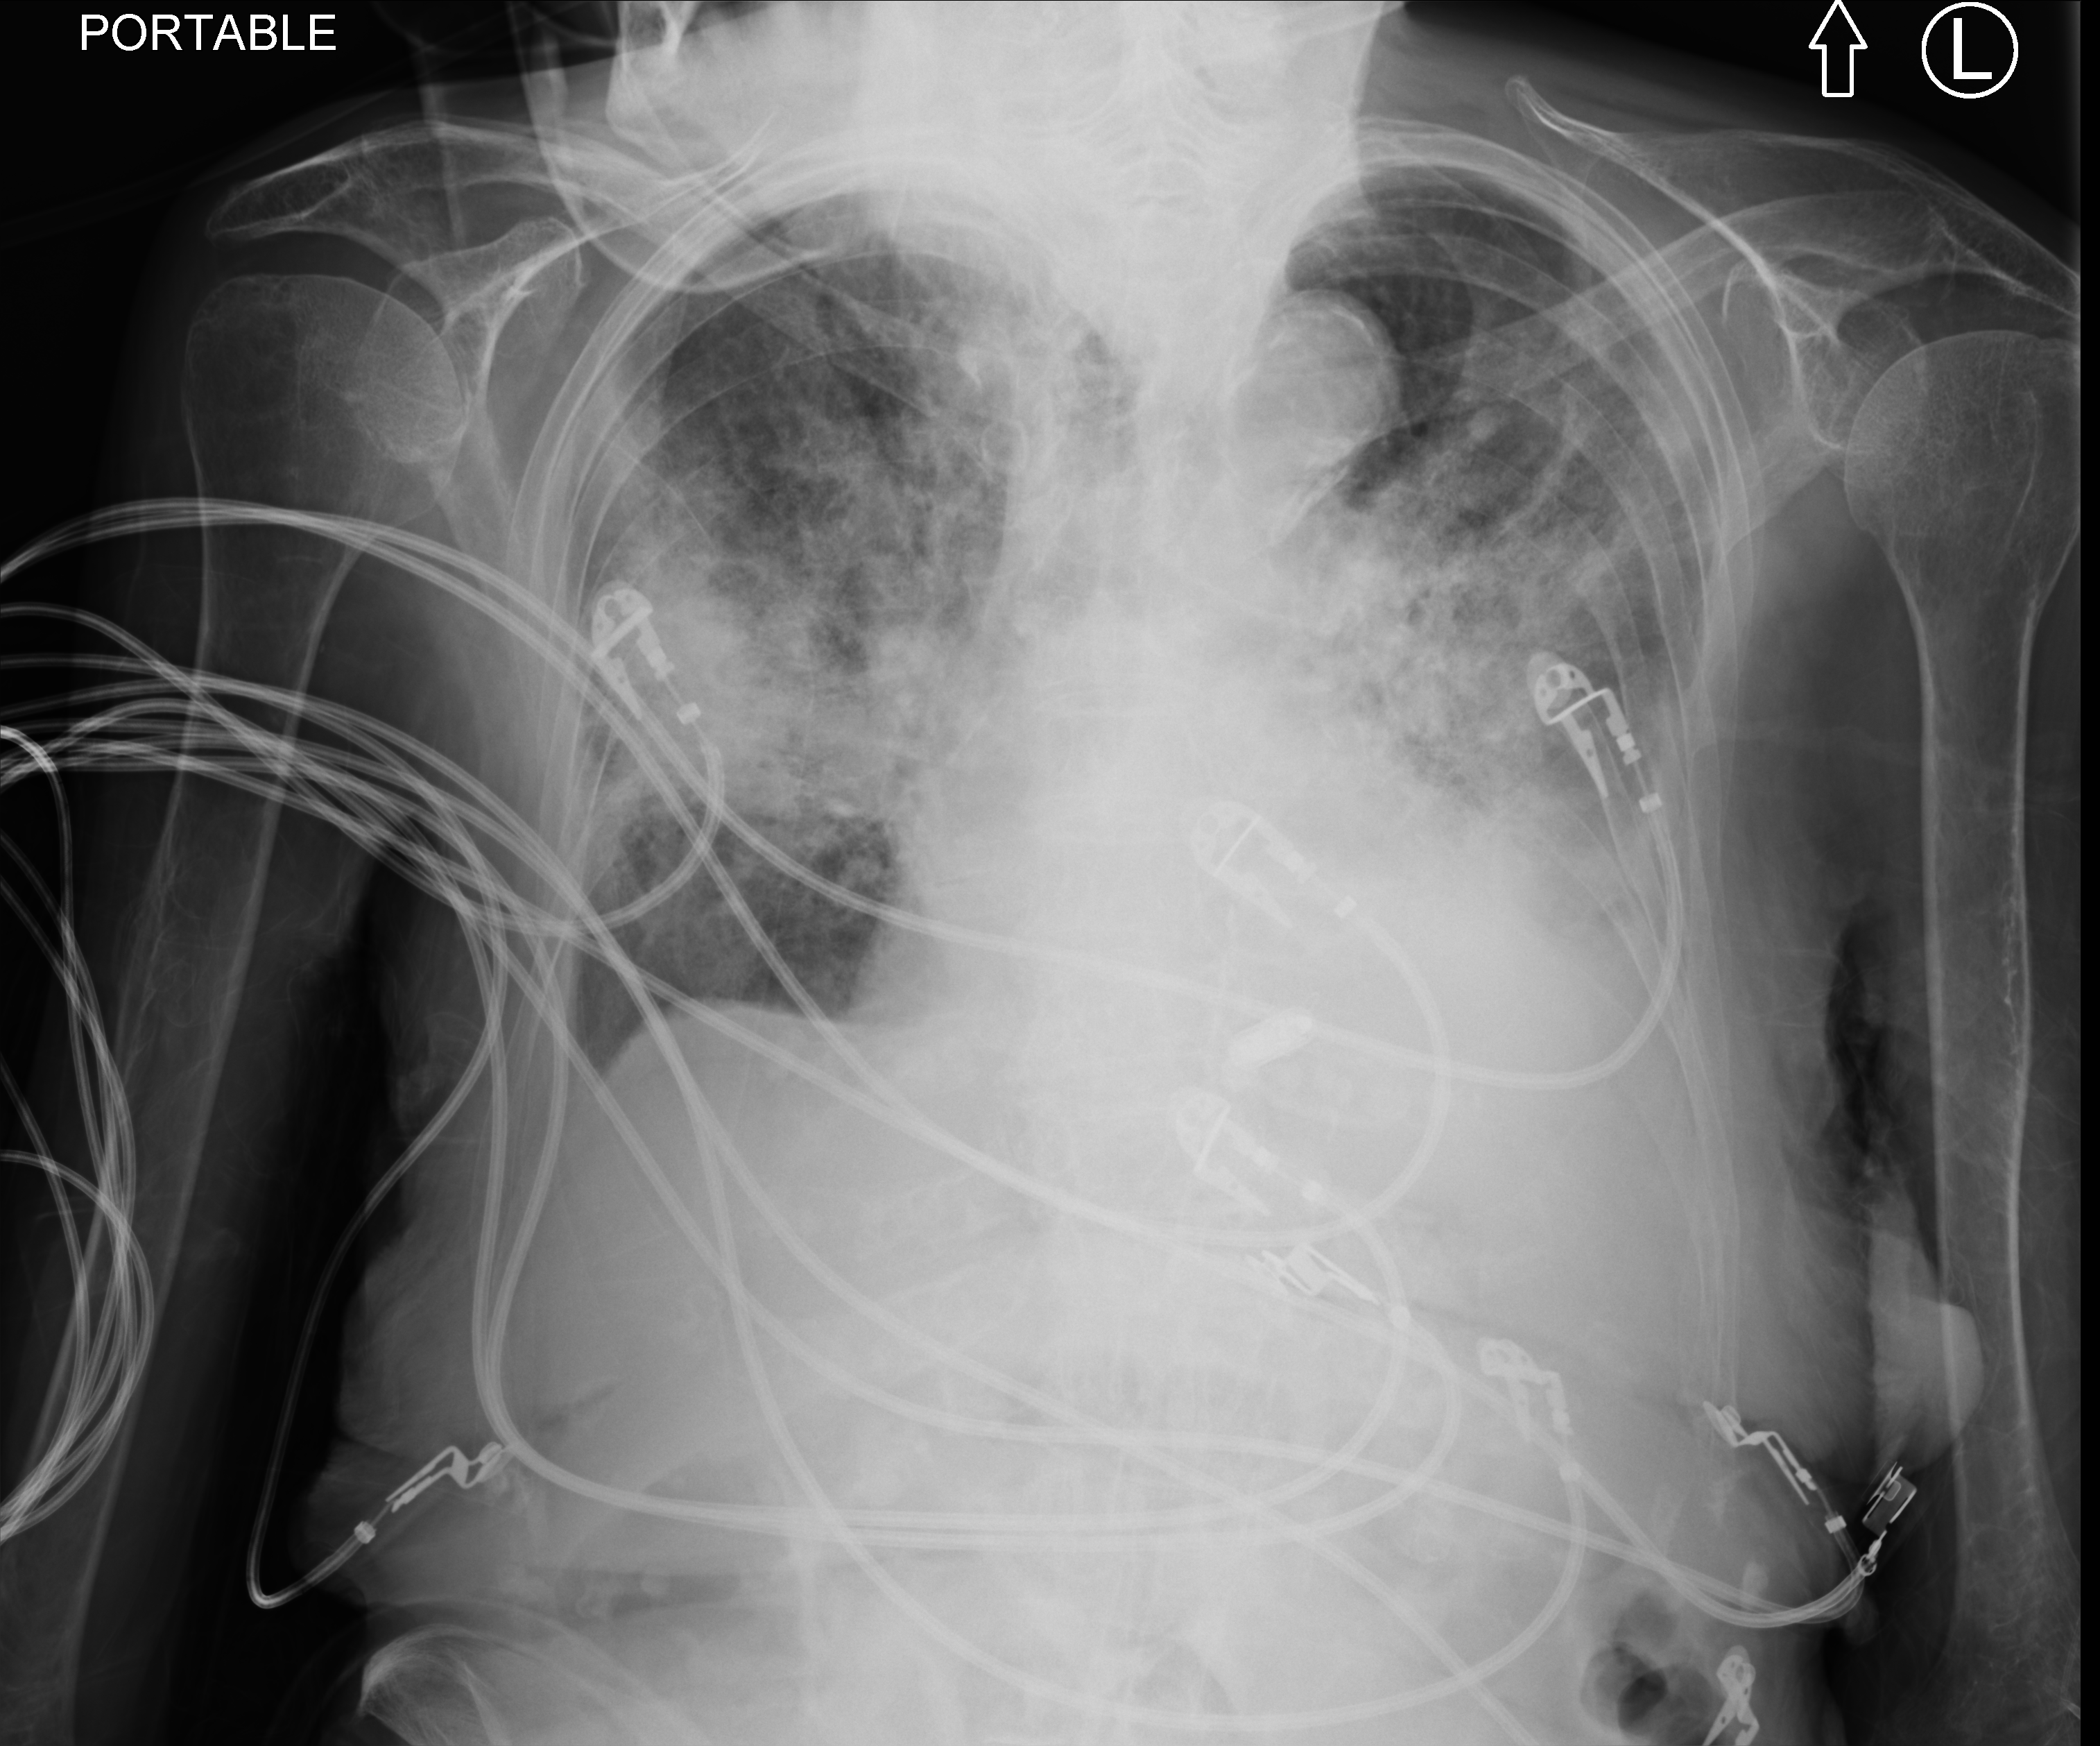
Portable chest radiograph, anteroposterior (AP) projection. Patient hospitalised with COVID-19; female, aged 75–90 years.
Admission-level facts for this patient (not findings on this image; timing relative to this image not recorded): admitted to intensive care during this hospital stay: no.